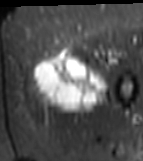
MRI of an extremity soft-tissue mass, one axial slice. STIR. MR volume resampled by the dataset authors to the PET/CT grid (not the native acquisition matrix). 143 × 161 image matrix. Female patient. From the clinical record (not read from this slice): histological type: myxofibrosarcoma; grade: intermediate; site of the primary tumour: left thigh.
Annotated regions visible in this slice (expert contour drawn on MRI and transferred to this co-registered scan by the dataset authors):
- gross tumour volume including surrounding oedema: bounding box [x1, y1, x2, y2] px = [29, 46, 111, 114]
- gross tumour volume (mass): [33, 49, 109, 114]